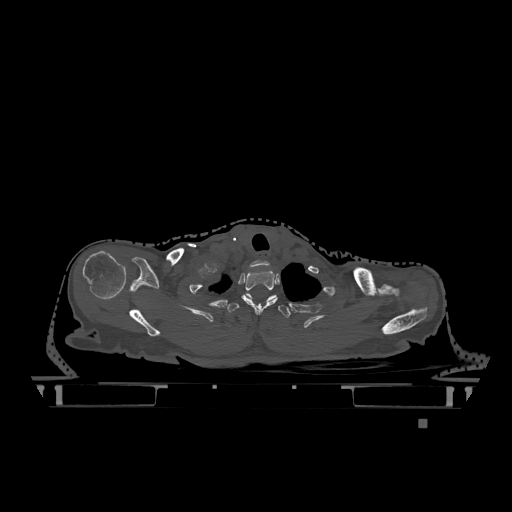
CT including the spine, one axial slice; position 989 of 1317 along the scan axis; bone window (W 1800 / L 400 HU); 0.5 mm slice thickness; 512 × 512 image matrix, field of view 500 × 500 mm. Female patient, age 74 years. Case-level facts recorded for this patient, not image findings: primary cancer: lung; vertebrae with lytic lesions (as recorded): T1, T4, T5, T6, L4, L5.
Structures marked on this image (semi-automatic segmentation, software-assisted and operator-edited):
- T1 vertebra: bounding box [x1, y1, x2, y2] px = [242, 270, 278, 314]
- T2 vertebra: [227, 294, 291, 318]